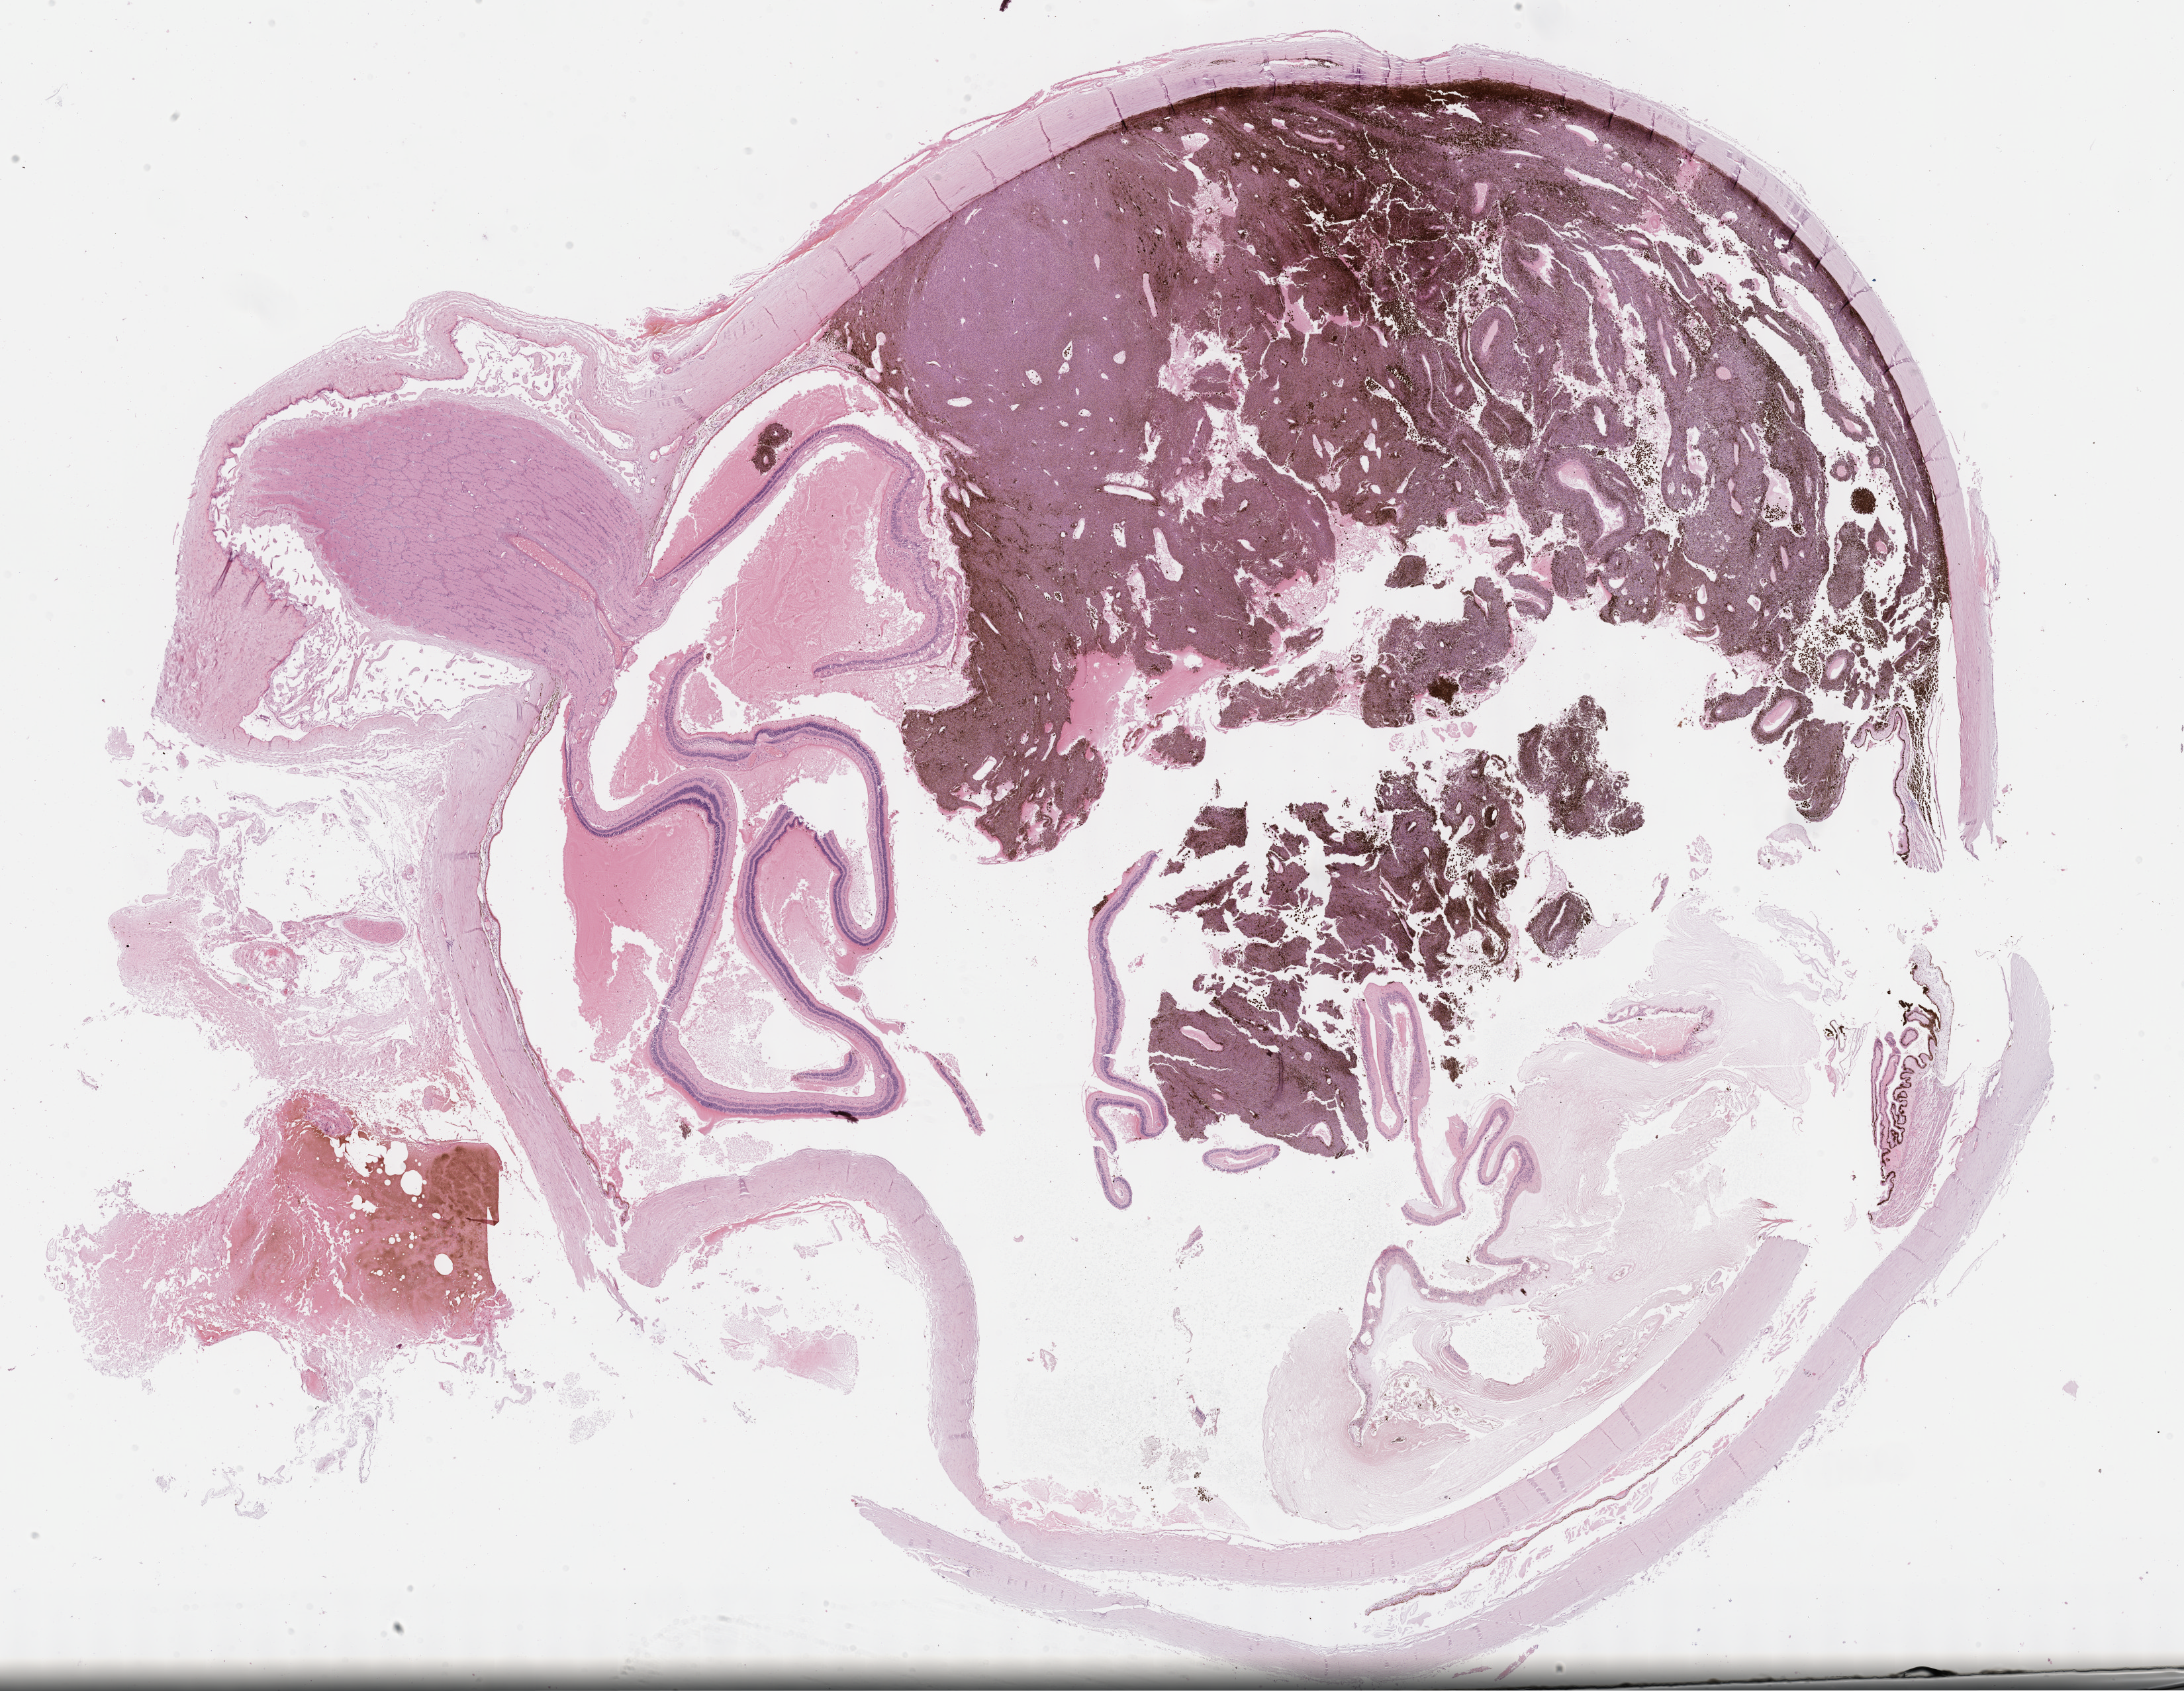
H&E whole-slide image, a low-resolution overview of the entire scanned area, about 26.7 x 20.7 mm (acquisition: 40x scan); formalin-fixed paraffin-embedded (FFPE) diagnostic section; primary tumour sample from the uvea. Female patient; age at initial diagnosis 78 years.
* AJCC pathologic stage: IIB (7th edition)
* diagnosis: Mixed epithelioid and spindle cell melanoma (choroid)
* laterality: right